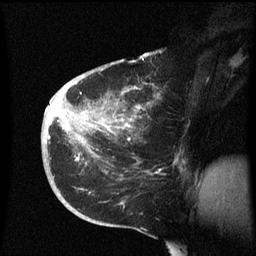
Breast MRI (dynamic contrast-enhanced), one sagittal slice. Dynamic contrast-enhanced series, image 2 of 3 at this slice position (ordered by acquisition). 1.5 T. TE 4.2 ms, TR 8.4 ms. 2.3 mm slice thickness. 256 × 256 image matrix. Female patient, age 38 years. From the clinical record (not read from this slice): setting: breast cancer imaged before/during neoadjuvant chemotherapy; receptor status: HER2-positive.
Annotated regions visible in this slice (semi-automatic segmentation, software-assisted and operator-edited):
- analysis volume of interest (the breast-tissue region the enhancement analysis was run in; not a lesion): bounding box <41,78,175,213> (left, top, right, bottom; pixels)
- tumour enhancement mask (voxels above the 70 % enhancement threshold inside the analysis volume of interest): <48,106,140,161>